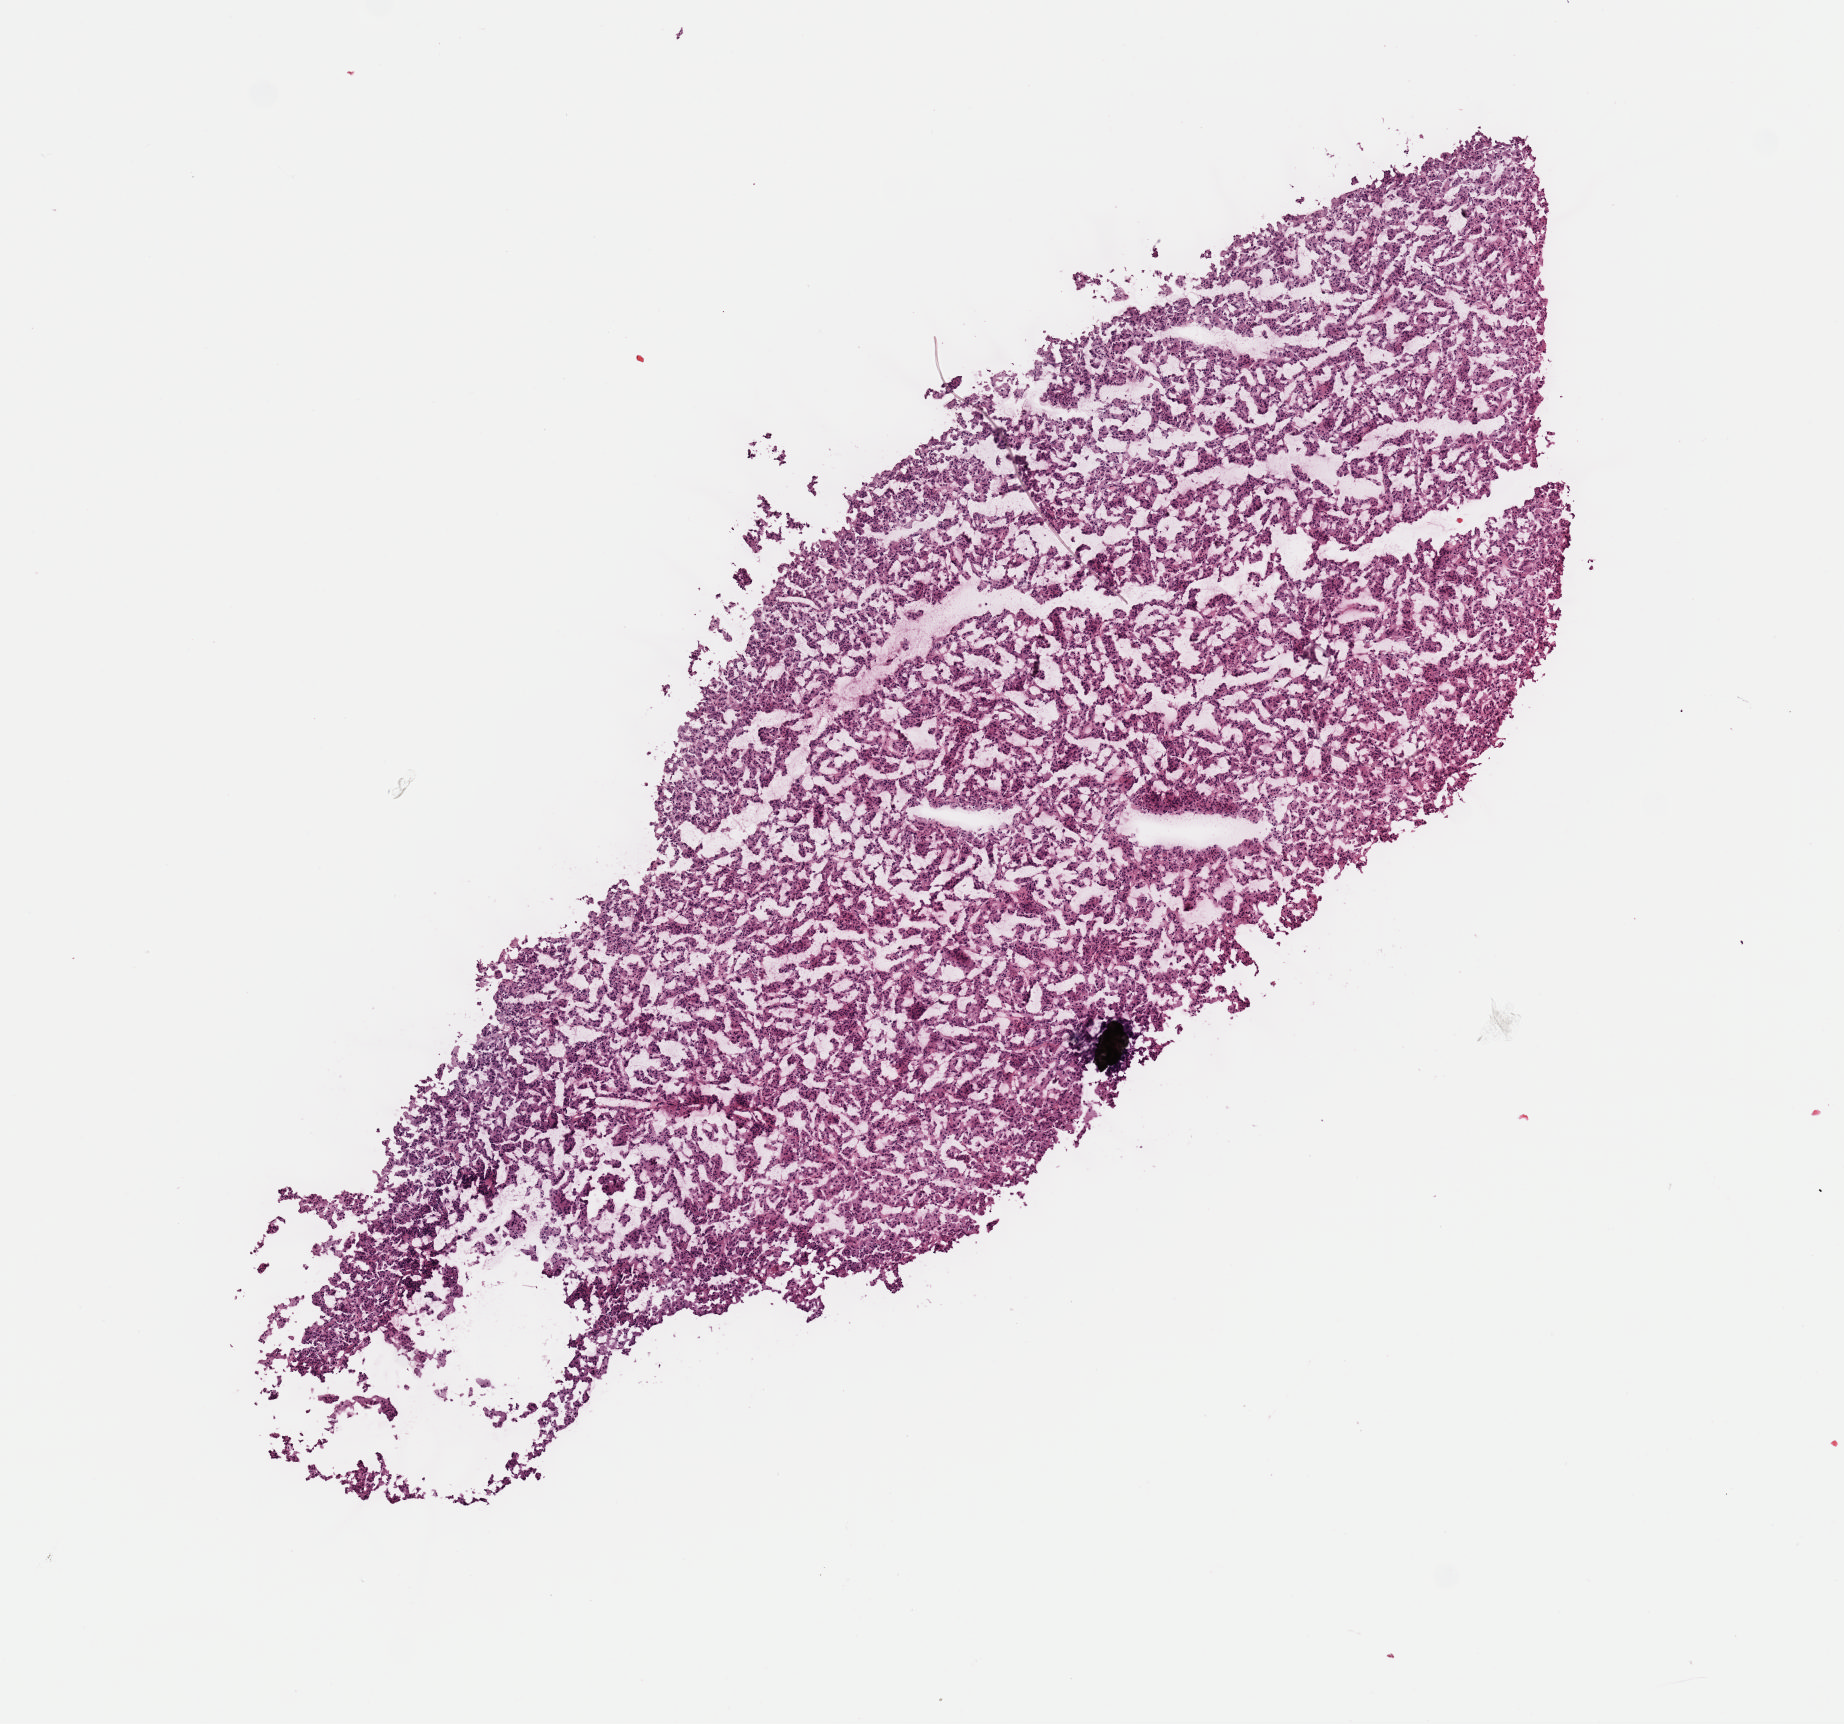
H&E-stained whole-slide image, low-resolution overview of the scanned area, about 7.3 x 6.8 mm (from a 40x scan), frozen section, sample: primary tumour, adrenal gland. Female, age 45 years at initial diagnosis. Slide review estimates, as recorded: tumour cells 100%, tumour nuclei 80%, normal cells 0%, stromal cells 0%, necrosis 0%. Infiltration values recorded for this section: lymphocyte infiltration 1%, monocyte infiltration 0%, neutrophil infiltration 0%.
Histologic diagnosis: Pheochromocytoma, NOS.